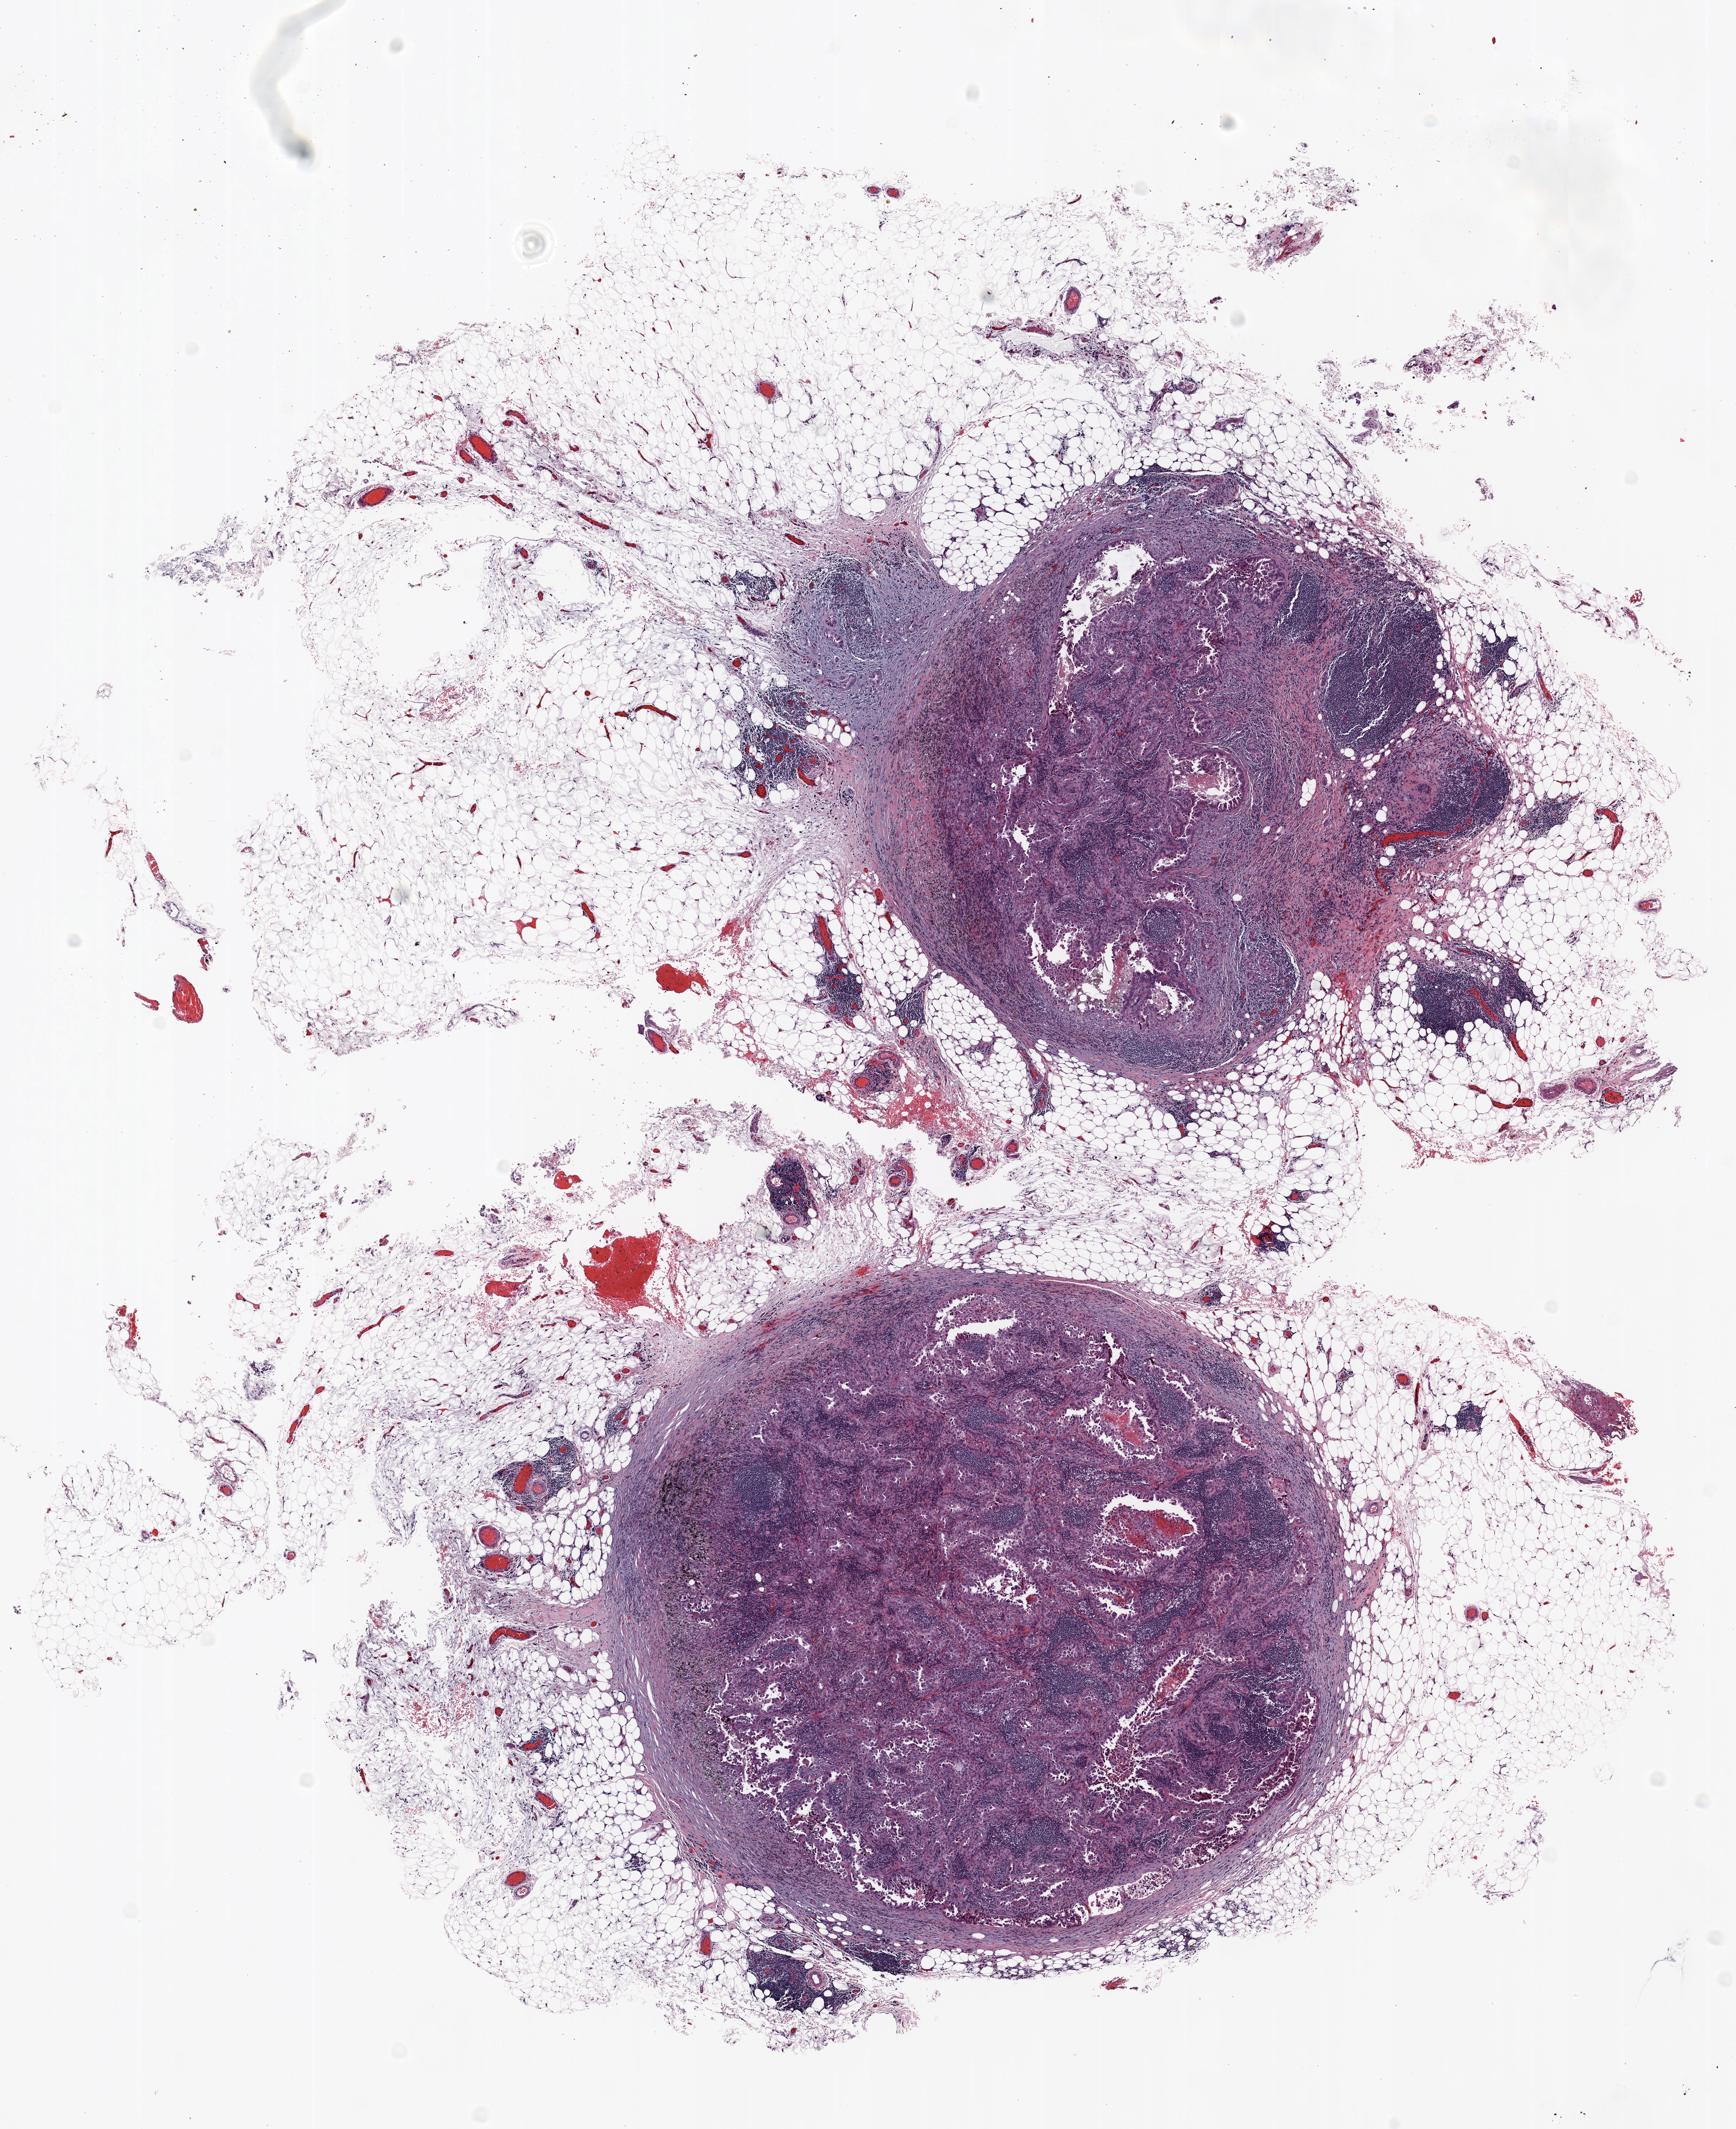
H&E-stained whole-slide image, whole scanned area (about 10.0 x 12.3 mm, from a 20x scan) shown as a low-resolution overview; FFPE section; lung. Female, age 73 at enrolment.
Participant's lung-cancer diagnosis: Adenocarcinoma, NOS.